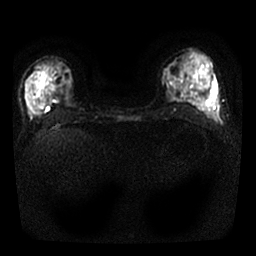
Breast MRI, one axial slice; slice 12 of 25 in the series (ordered by position); diffusion-weighted series; image 2 of 4 stored at this slice position (different b-values; order by instance number); 1.5 T; 4 mm slice thickness; 256 × 256 image matrix. Female patient.
Outlined on this slice (outlined manually by an expert reader):
- tumour on diffusion-weighted imaging: bounding box (x1, y1, x2, y2) in pixels: (28, 104, 35, 114)